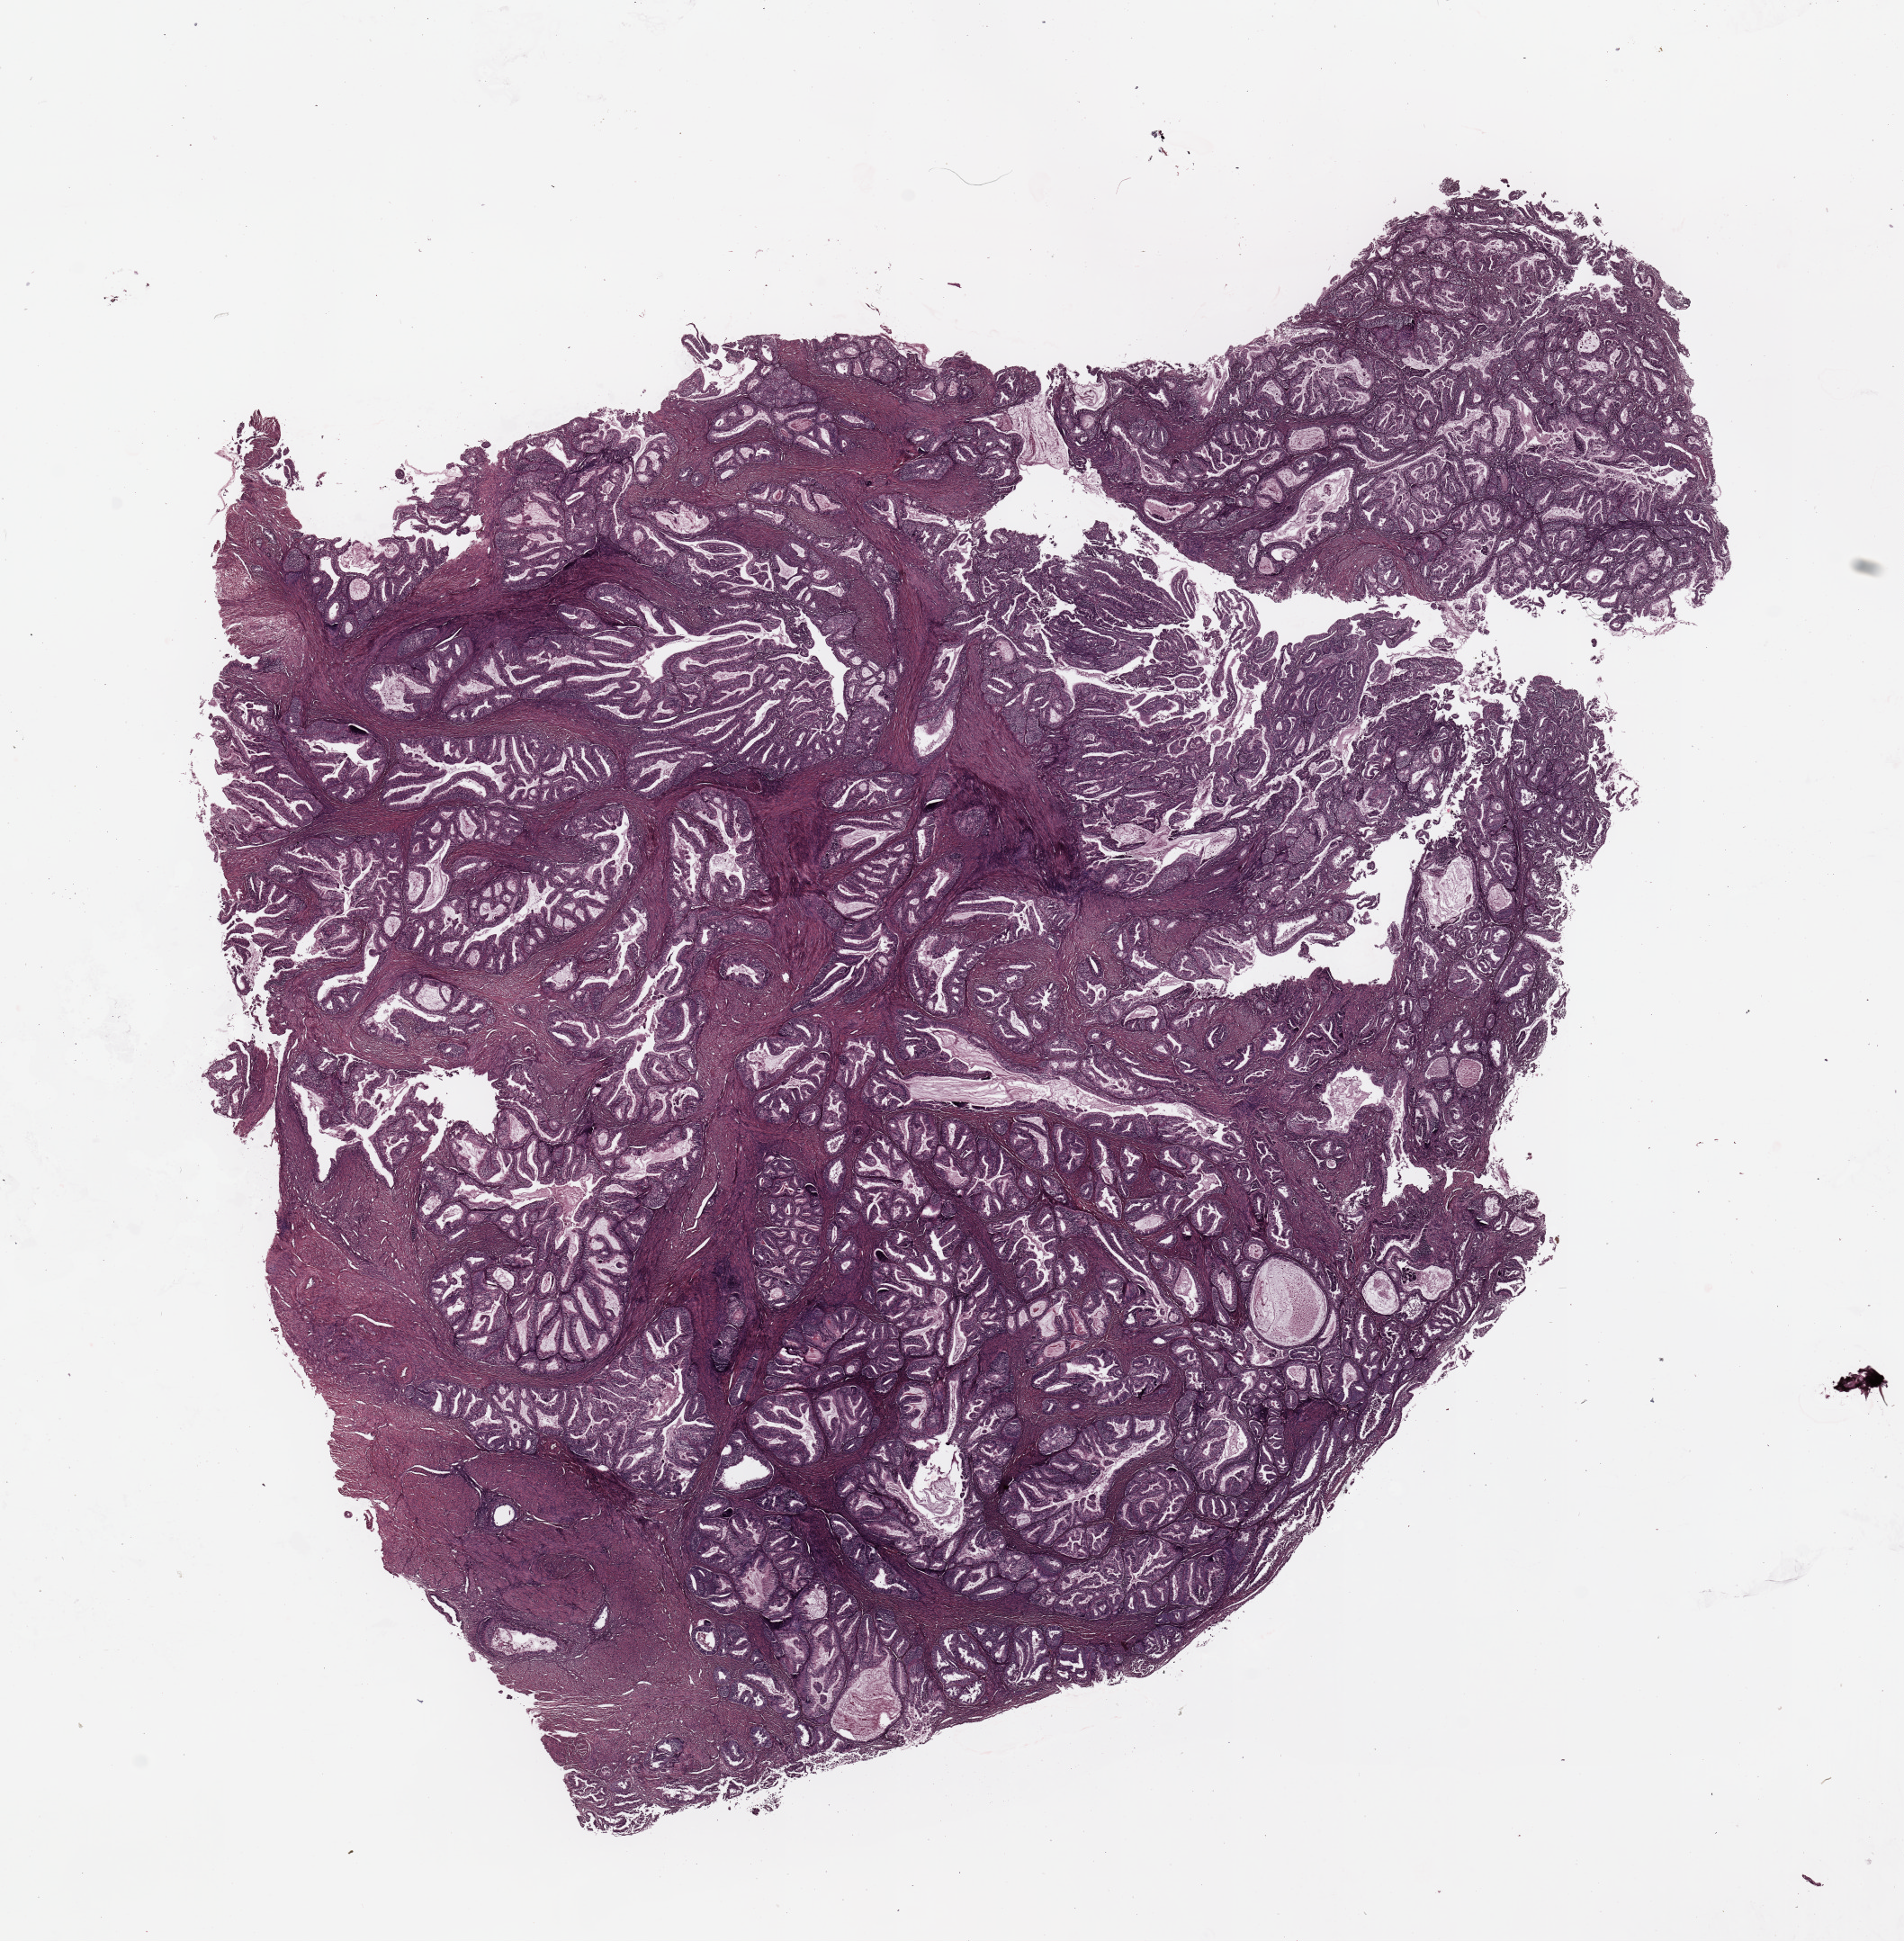
Whole-slide histology image, H&E-stained, whole scanned area (about 16.7 x 17.1 mm) shown as a low-resolution overview, tumour tissue sample, sampled site: uterus. 58-year-old female patient. Histologic grade: G1 (well differentiated). Composition of this section per pathologist review: tumour nuclei 90%, necrosis 0%.
• AJCC pathologic stage: I
• histologic diagnosis: Endometrioid adenocarcinoma, NOS